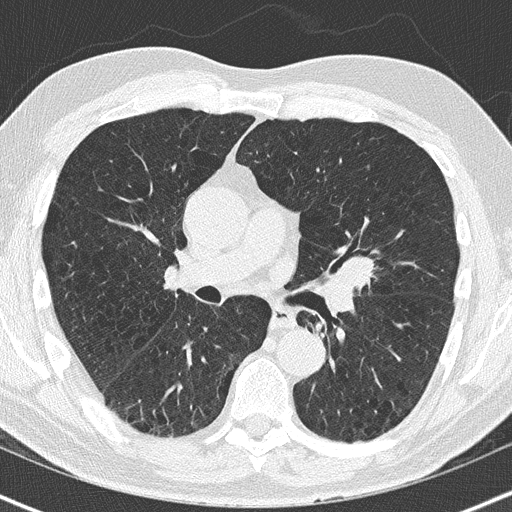
Chest CT (low-dose screening protocol), one axial image, baseline screening round, lung window (W 1500 / L -600 HU), slice 75 of 163 in the series. Male participant, aged 63 years at enrolment. Former smoker at enrolment.
Expert reader's lesion annotation, bounding box [x1, y1, x2, y2] px = [332, 253, 377, 291]. The screening reader recorded 2 non-calcified nodules or masses ≥4 mm on this exam (lingula, right lower lobe); which of them this box marks is not recorded. Lung cancer was diagnosed 32 days after this screen: squamous cell carcinoma, NOS, left upper lobe, moderately differentiated (G2), stage IA (AJCC 6th edition), 23 mm at pathology.